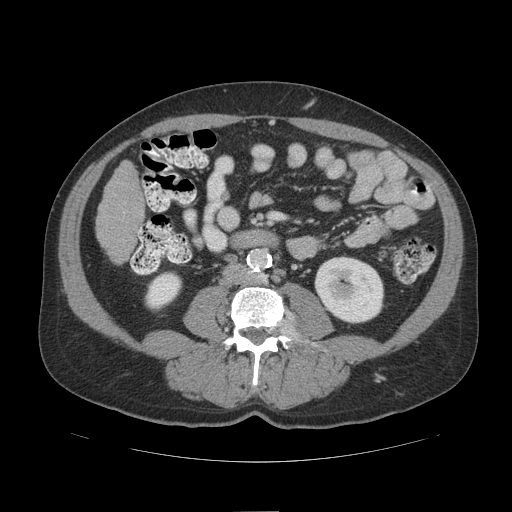
Contrast-enhanced abdominal CT (liver protocol), one axial slice. Slice 27 of 109 in the series (ordered by position). 140 kVp. Soft-tissue window (W 400 / L 40 HU). 512 × 512 image matrix, field of view 420 × 420 mm. Case-level facts recorded for this patient, not image findings: diagnosis: hepatocellular carcinoma (patient treated with transarterial chemoembolisation; whether this scan precedes or follows treatment is not stated here); TNM stage (as recorded): Stage-IIIB; Child-Pugh class: A; tumour differentiation: poorly differentiated; tumour nodularity: multinodular.
Annotated regions visible in this slice (semi-automatic segmentation, software-assisted and operator-edited):
- liver parenchyma outside the tumour (the mass and vessels are separate outlines, so this box may not span the whole liver): bounding box (x1, y1, x2, y2) in pixels: (96, 160, 144, 262)